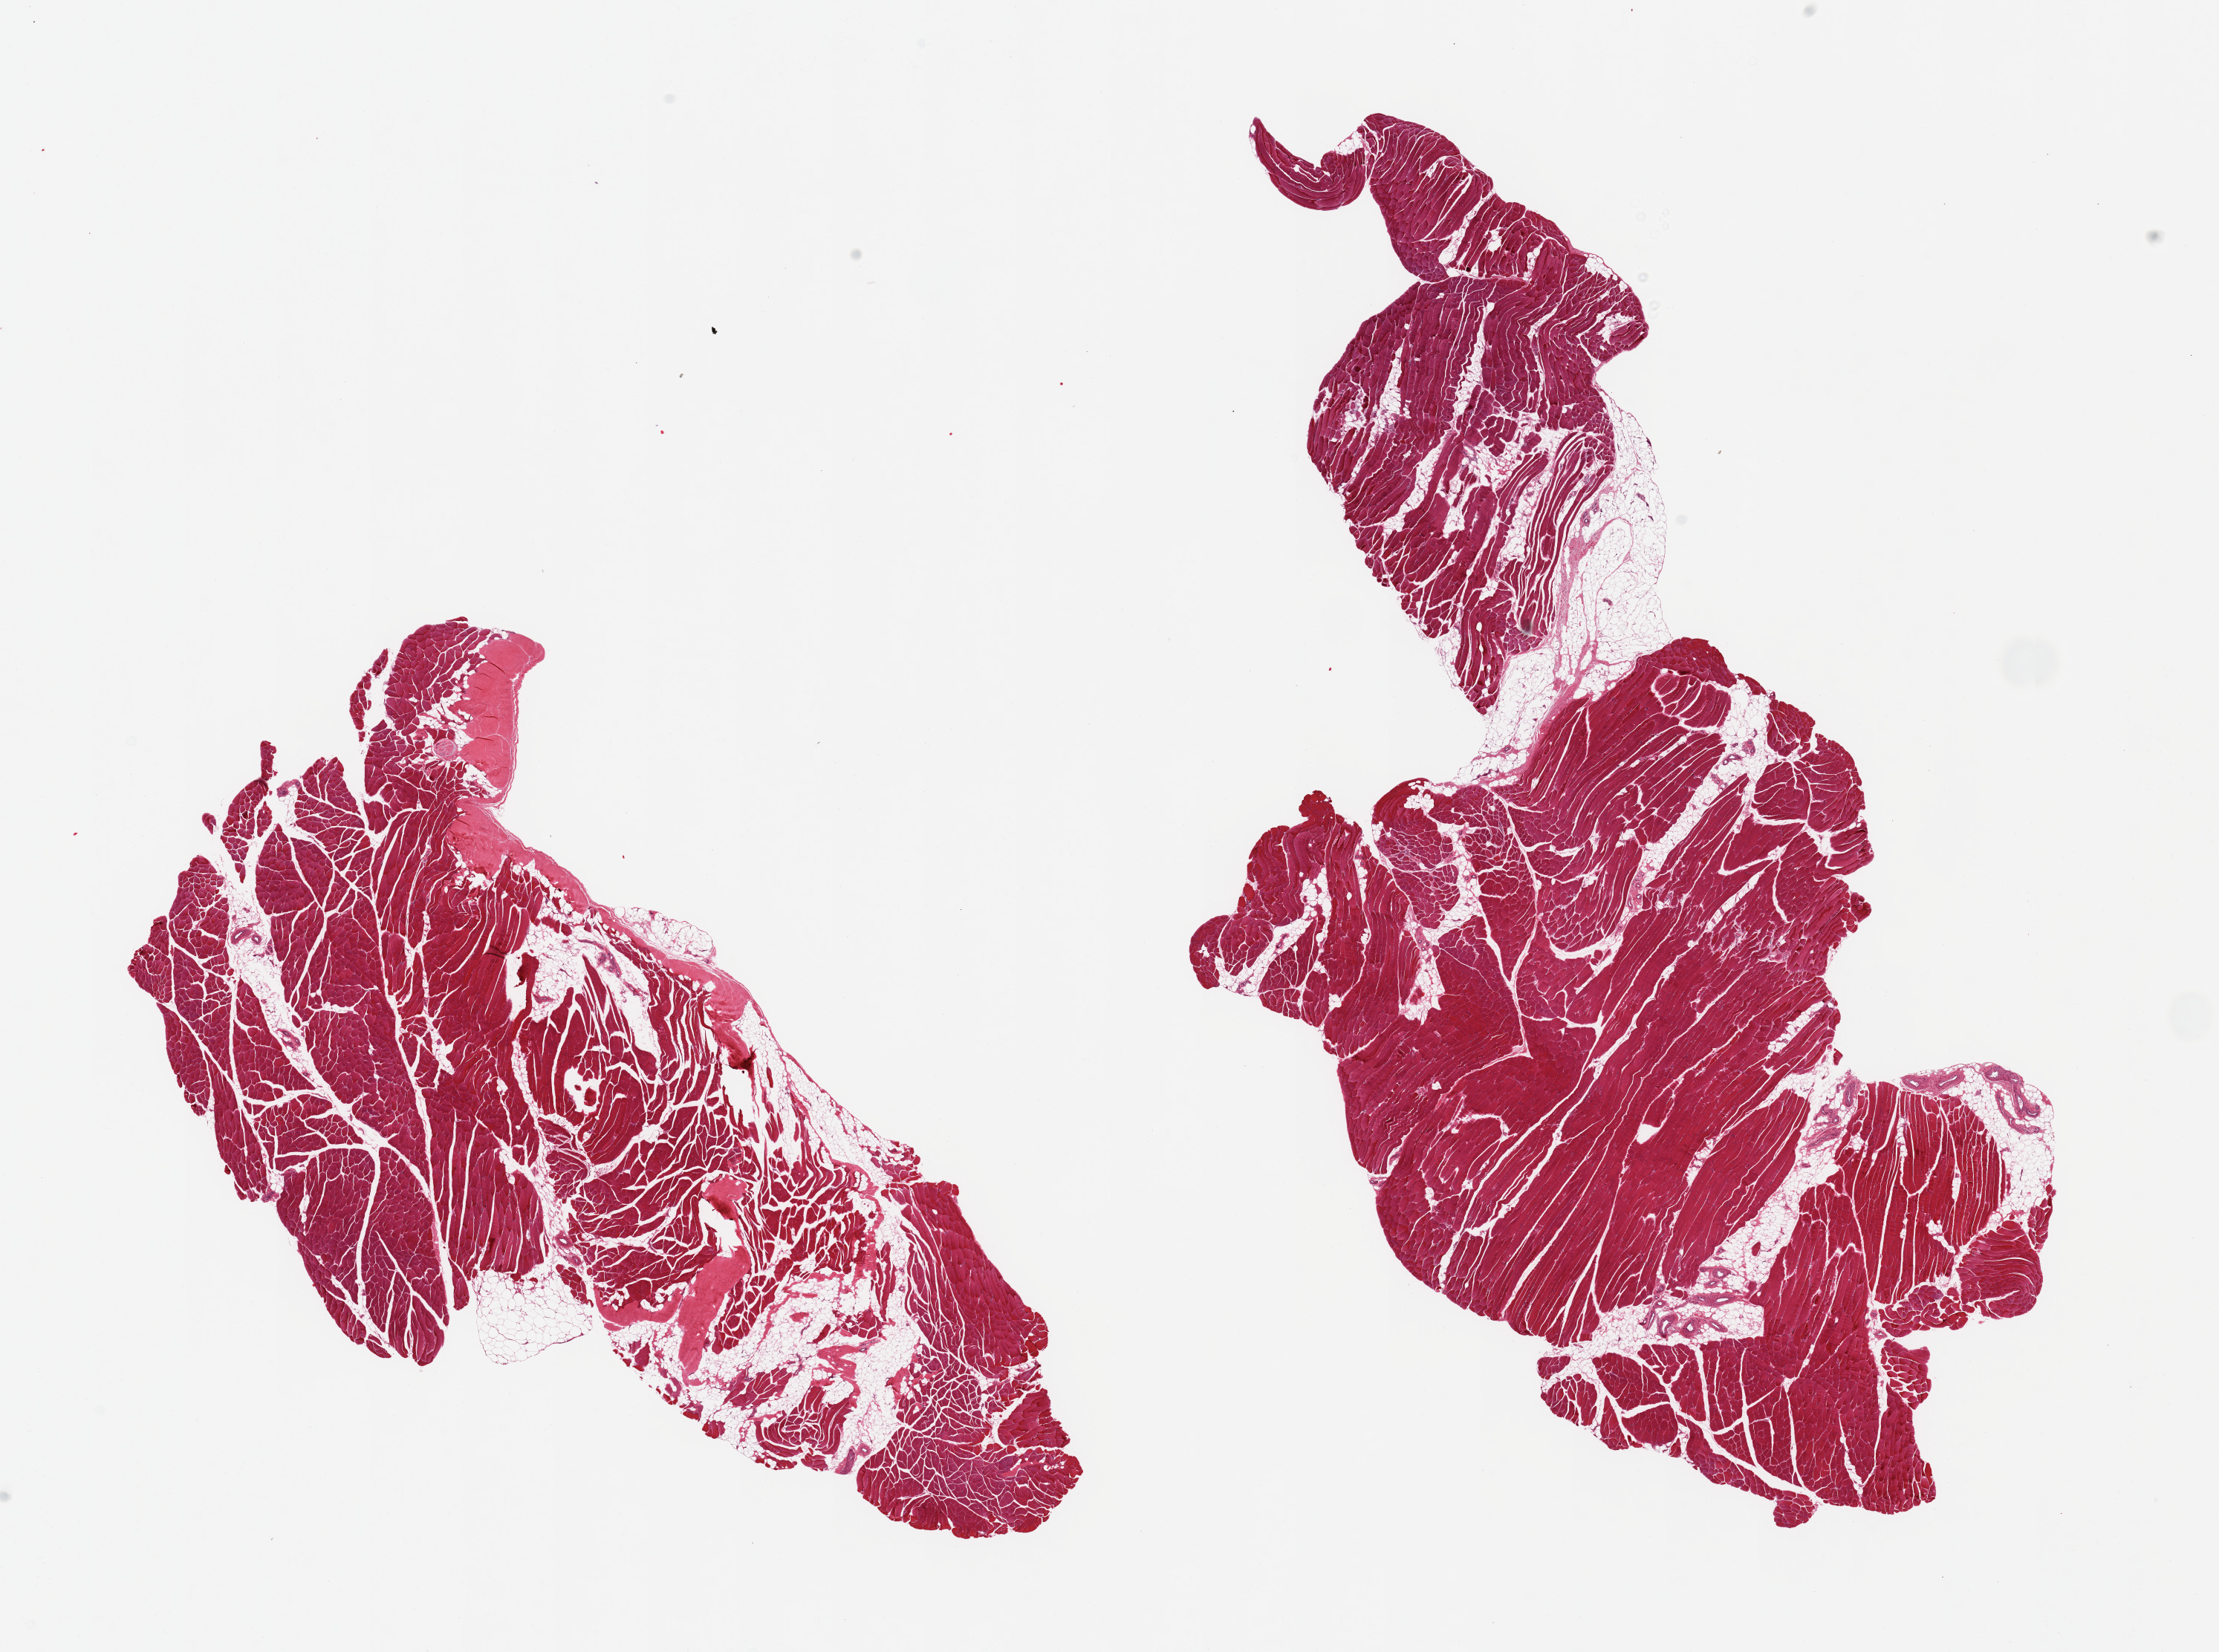
Digitized hematoxylin and eosin (H&E)-stained section, whole scanned area (about 23.6 x 17.6 mm, slide scanned at 20x) shown as a low-resolution overview, PAXgene-fixed paraffin-embedded (PFPE) section, sampled site (target tissue): skeletal muscle, tissue donor sample. Female donor.
Review note (as recorded): 2 pieces ~20% interstitial fat.